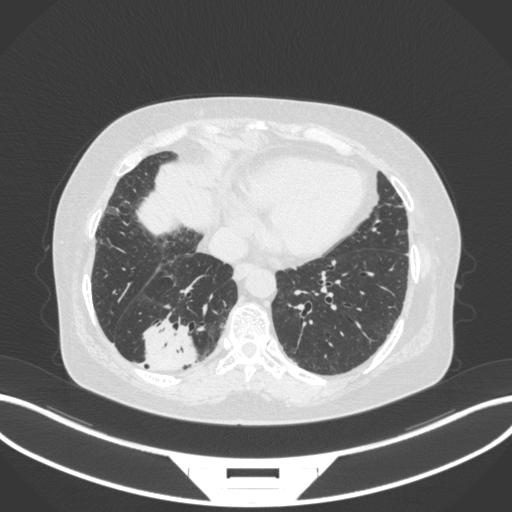
Chest CT, one axial slice. Slice 63 of 303 in the series (ordered by position). Reconstruction kernel B31f. Lung window (W 1500 / L -600 HU). 1 mm slice thickness. 512 × 512 image matrix, field of view 400 × 400 mm. Patient: female, 65 years. Case-level facts recorded for this patient, not image findings: clinical TNM (as recorded): T2b N1 M0.
Annotated regions visible in this slice (rectangle marked by the reading radiologist):
- lung tumour (recorded histology: adenocarcinoma): bounding box <136,315,200,374> (left, top, right, bottom; pixels)